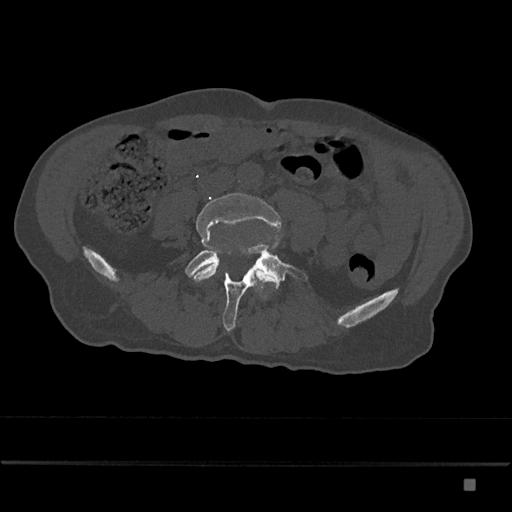
CT including the spine, one axial slice; position 303 of 797 along the scan axis; reconstruction kernel Br40s/3; bone window (W 1800 / L 400 HU); 0.5 mm slice thickness; 512 × 512 image matrix, field of view 390 × 390 mm. Patient: male, 72 years. Case-level facts recorded for this patient, not image findings: primary cancer: prostate.
Outlined on this slice (semi-automatic segmentation, software-assisted and operator-edited):
- L4 vertebra: box from (x=190, y=193) to (x=282, y=282) px
- L5 vertebra: (x=185, y=244)–(x=308, y=331)